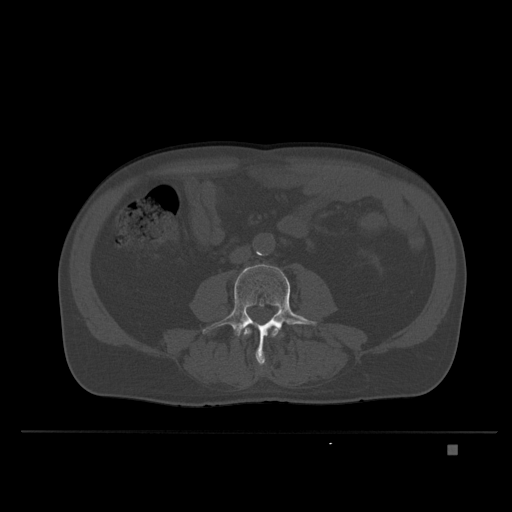
CT including the spine, one axial slice; slice 79 of 435 in the series (ordered by position); bone window (W 1800 / L 400 HU); 1.5 mm slice thickness; 512 × 512 image matrix, field of view 434 × 434 mm. Patient: male, 73 years. Case-level facts recorded for this patient, not image findings: primary cancer: skin.
Annotated regions visible in this slice (semi-automatic segmentation, software-assisted and operator-edited):
- L3 vertebra: bounding box (x1, y1, x2, y2) in pixels: (243, 326, 278, 338)
- L4 vertebra: (202, 264, 317, 370)